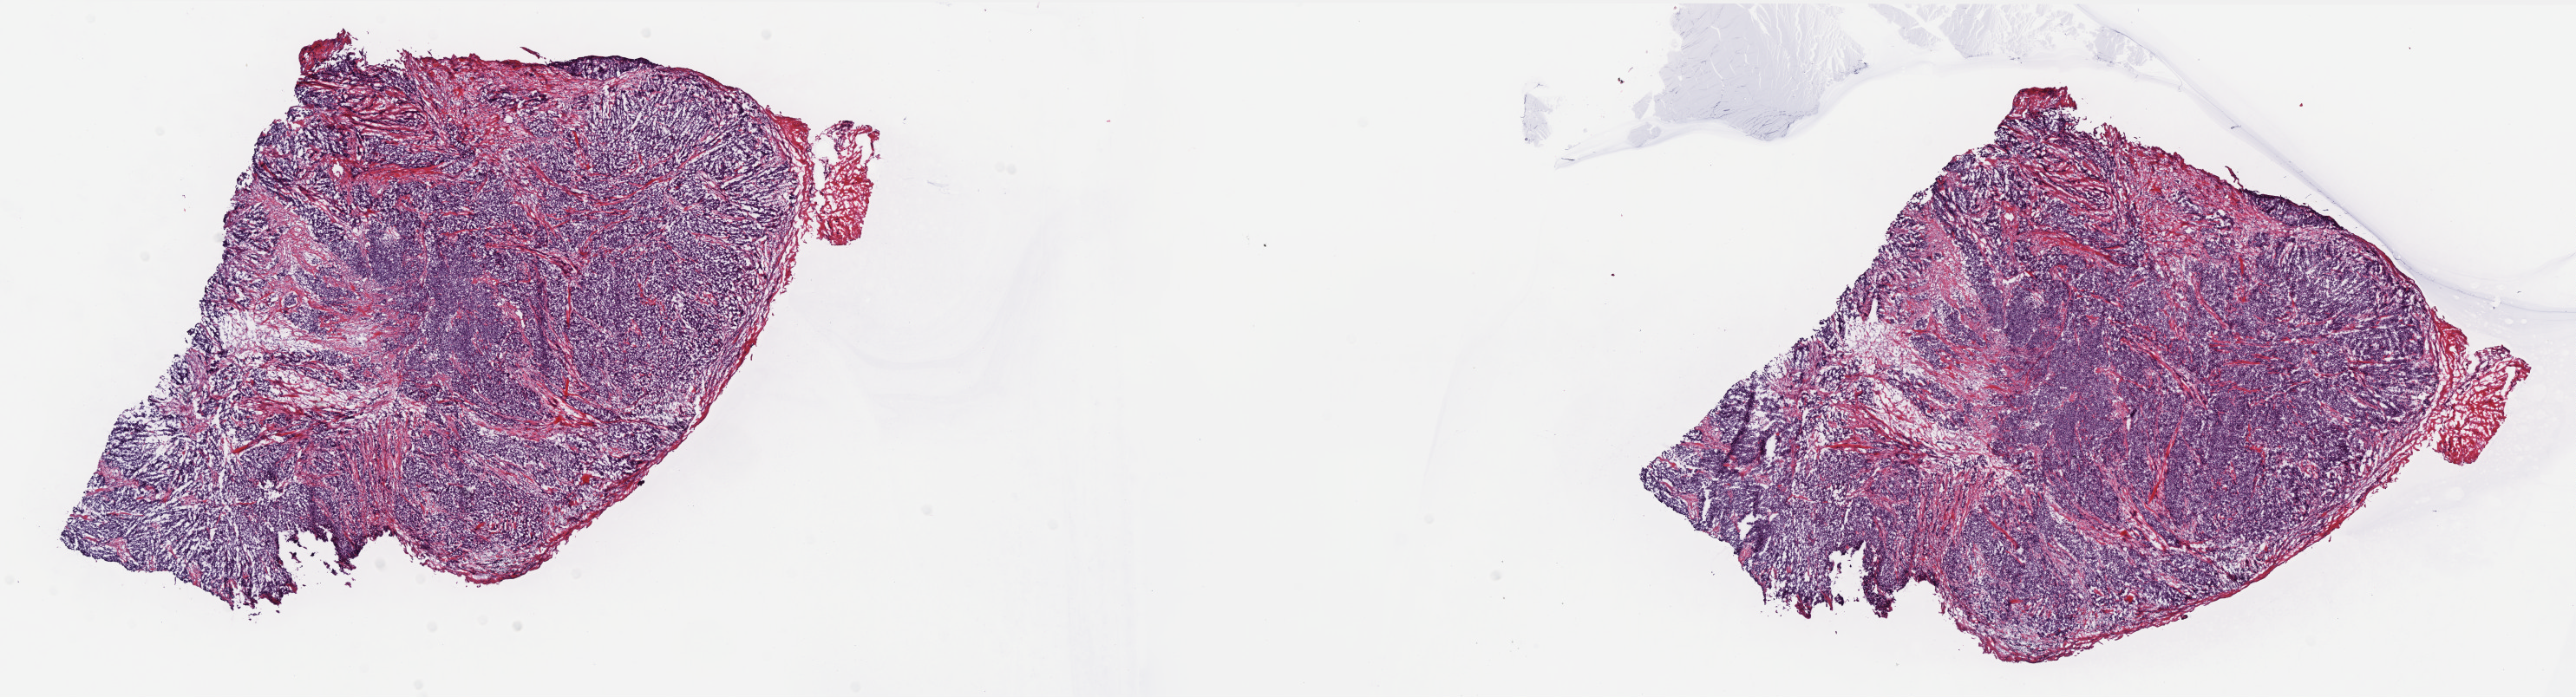
H&E whole-slide image, low-resolution overview of the scanned area, about 23.8 x 6.4 mm (from a 40x scan). Frozen section from the top of the tissue portion. Primary tumour sample from the breast. Female patient; age at initial diagnosis 55 years. Pathologist review of this section (percent, as recorded): tumour cells 85%, tumour nuclei 90%, normal cells 0%, stromal cells 12%, necrosis 3%. Inflammatory infiltration, as recorded: lymphocyte infiltration 4%, monocyte infiltration 0%, neutrophil infiltration 0%.
Lymph nodes positive (case pathology): 0 of 17 examined. Pathologic diagnosis: Infiltrating duct carcinoma, NOS. AJCC pathologic stage: IIA. Laterality: right. TNM: T2 N0 M0.